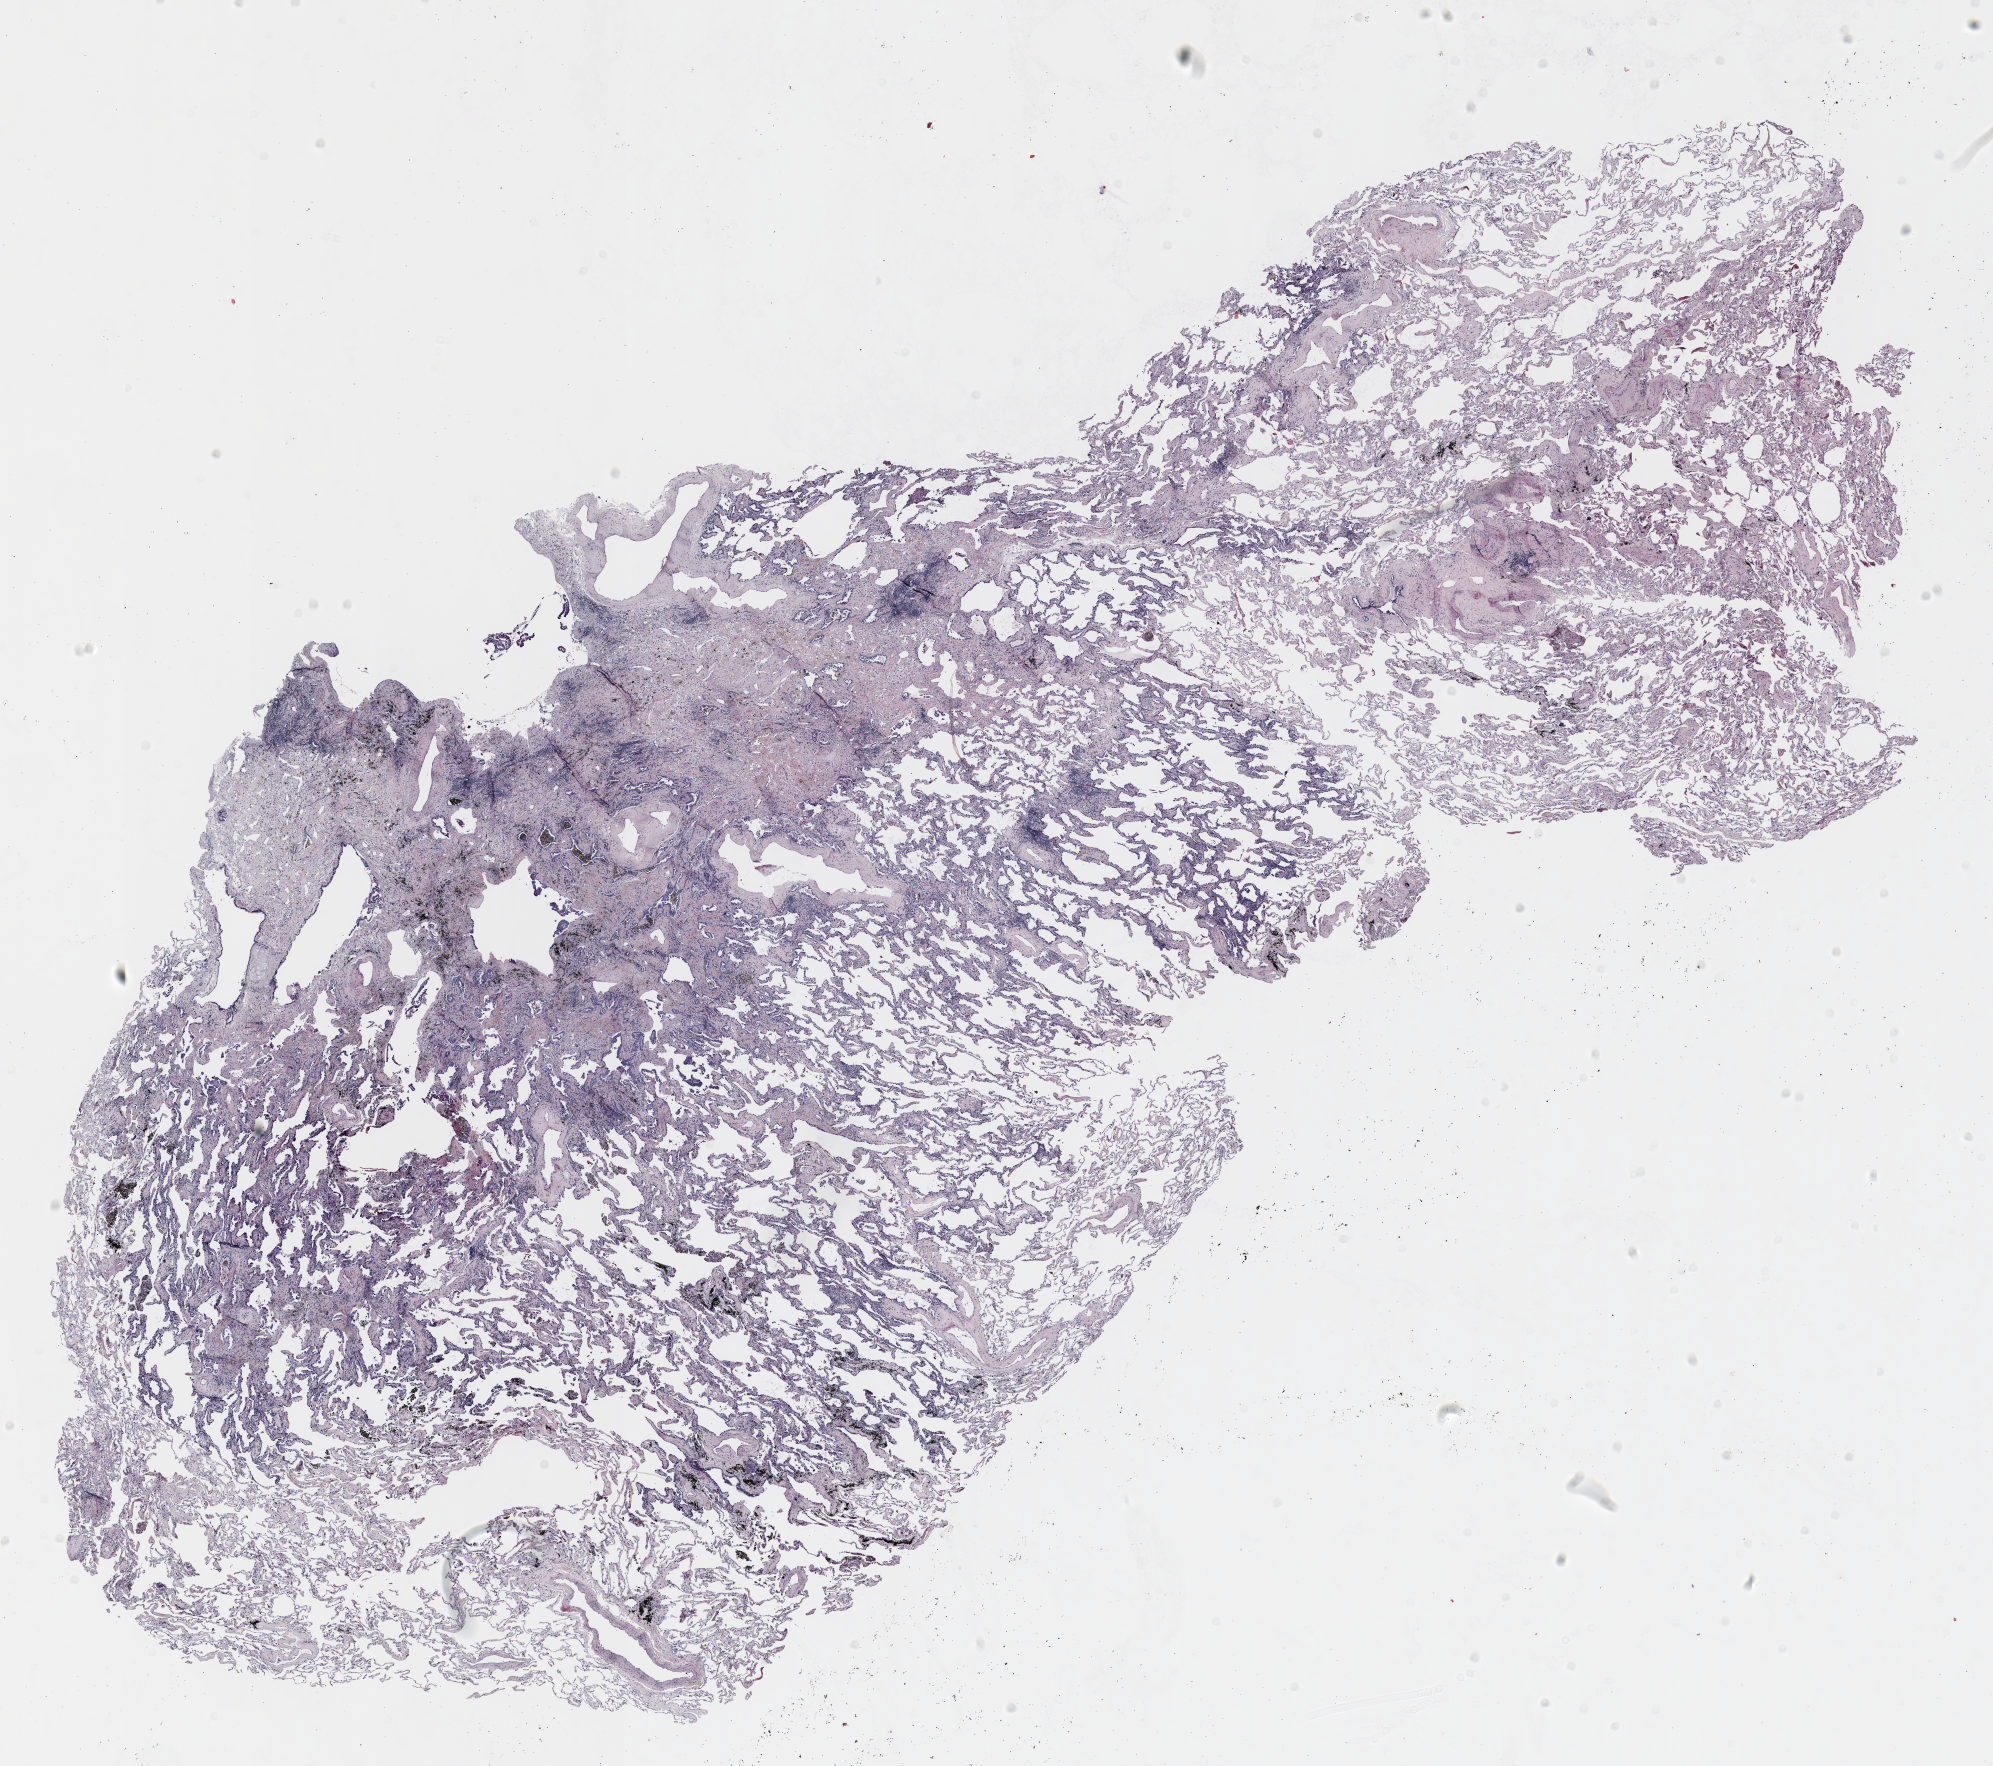
Whole-slide histology image, Hematoxylin and eosin (H&E) stained — shown as a low-resolution overview of the whole scanned area (about 16.0 x 14.2 mm, slide scanned at 20x); formalin-fixed paraffin-embedded (FFPE) section; lung tissue. Female patient, aged 58 at enrolment. Current smoker at enrolment. Grade: moderately differentiated (G2).
ICD-O-3 topography: upper lobe of lung (C34.1). Primary tumour location (clinical record): right upper lobe. Stage (AJCC 6th edition): IA. Participant's lung-cancer diagnosis: Bronchiolo-alveolar adenocarcinoma, NOS. Tumour size (pathology): 7 mm.